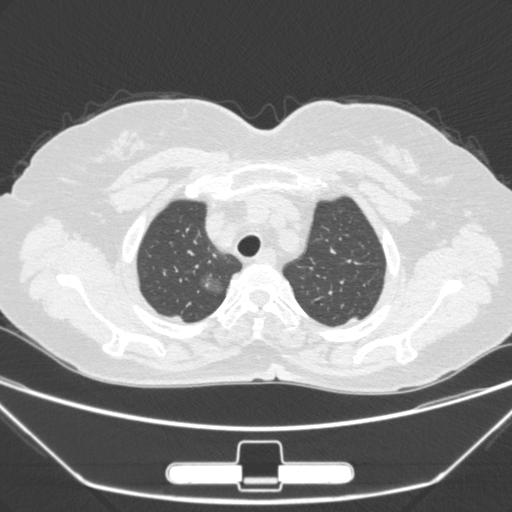
Chest CT, one axial slice. Position 233 of 275 along the scan axis. 120 kVp. Lung window (W 1500 / L -600 HU). 1 mm slice thickness. 512 × 512 image matrix, field of view 356 × 356 mm. Female patient, age 63 years. From the clinical record (not read from this slice): clinical TNM (as recorded): T1a N0 M0; histopathological grade: G1.
Outlined on this slice (rectangle marked by the reading radiologist):
- lung tumour (recorded histology: adenocarcinoma): bounding box <193,270,223,303> (left, top, right, bottom; pixels)